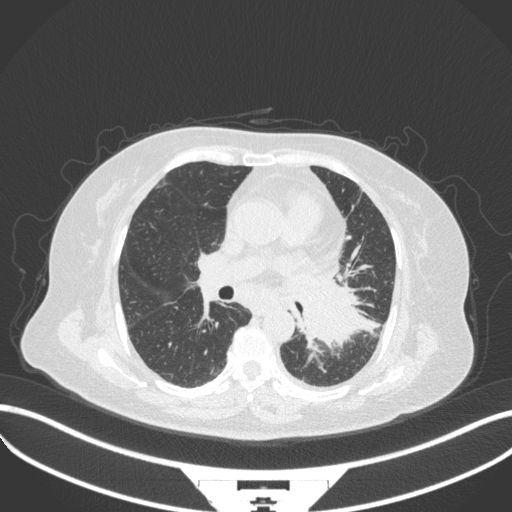
Chest CT, one axial slice. Reconstruction kernel B31f. Lung window (W 1500 / L -600 HU). 1 mm slice thickness. 512 × 512 image matrix, field of view 400 × 400 mm. Female patient, age 69 years. Case-level facts recorded for this patient, not image findings: clinical TNM (as recorded): T2b N3 M1.
Annotated regions visible in this slice (bounding box drawn by a radiologist):
- lung tumour (recorded histology: adenocarcinoma): bounding box <297,274,374,358> (left, top, right, bottom; pixels)